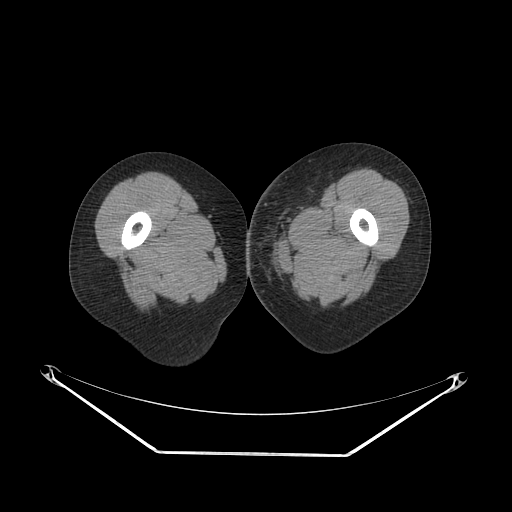
CT of an extremity soft-tissue mass (from a PET/CT study), one axial slice. Slice 38 of 267 in the series (ordered by position). Reconstruction kernel SOFT. 140 kVp. Soft-tissue window (W 400 / L 40 HU). 3.75 mm slice thickness. 512 × 512 image matrix, field of view 500 × 500 mm. Female patient. From the clinical record (not read from this slice): histological type: leiomyosarcoma; grade: high; site of the primary tumour: groin.
Outlined on this slice (expert contour drawn on MRI and transferred to this co-registered scan by the dataset authors):
- gross tumour volume including surrounding oedema: bounding box [x1, y1, x2, y2] px = [246, 205, 291, 250]